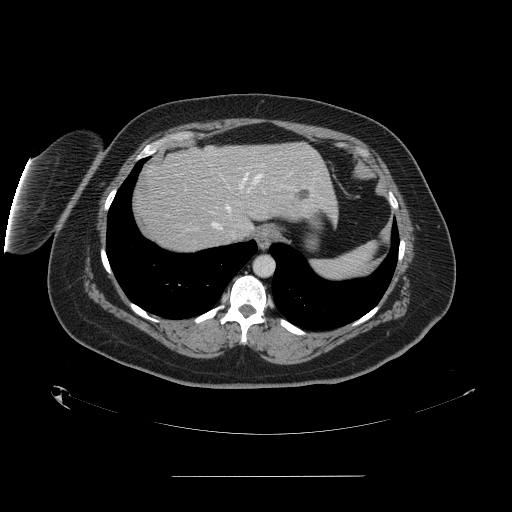
Contrast-enhanced abdominal CT, one axial slice; slice 129 of 164 in the series (ordered by position); 120 kVp; intravenous contrast given; soft-tissue window (W 400 / L 40 HU); 2.5 mm slice thickness; 512 × 512 image matrix. Female patient, age 52 years. From the clinical record (not read from this slice): diagnosis: colorectal cancer liver metastases, imaged before liver resection; multiple liver metastases: yes; largest metastasis: 3.5 cm; disease in both lobes: no.
Structures marked on this image (manually delineated by an expert):
- hepatic veins: bounding box <211,172,262,238> (left, top, right, bottom; pixels)
- liver: <136,143,336,254>
- planned liver remnant (the part of the liver to remain after resection): <172,143,336,229>
- liver metastasis: <300,191,309,200>